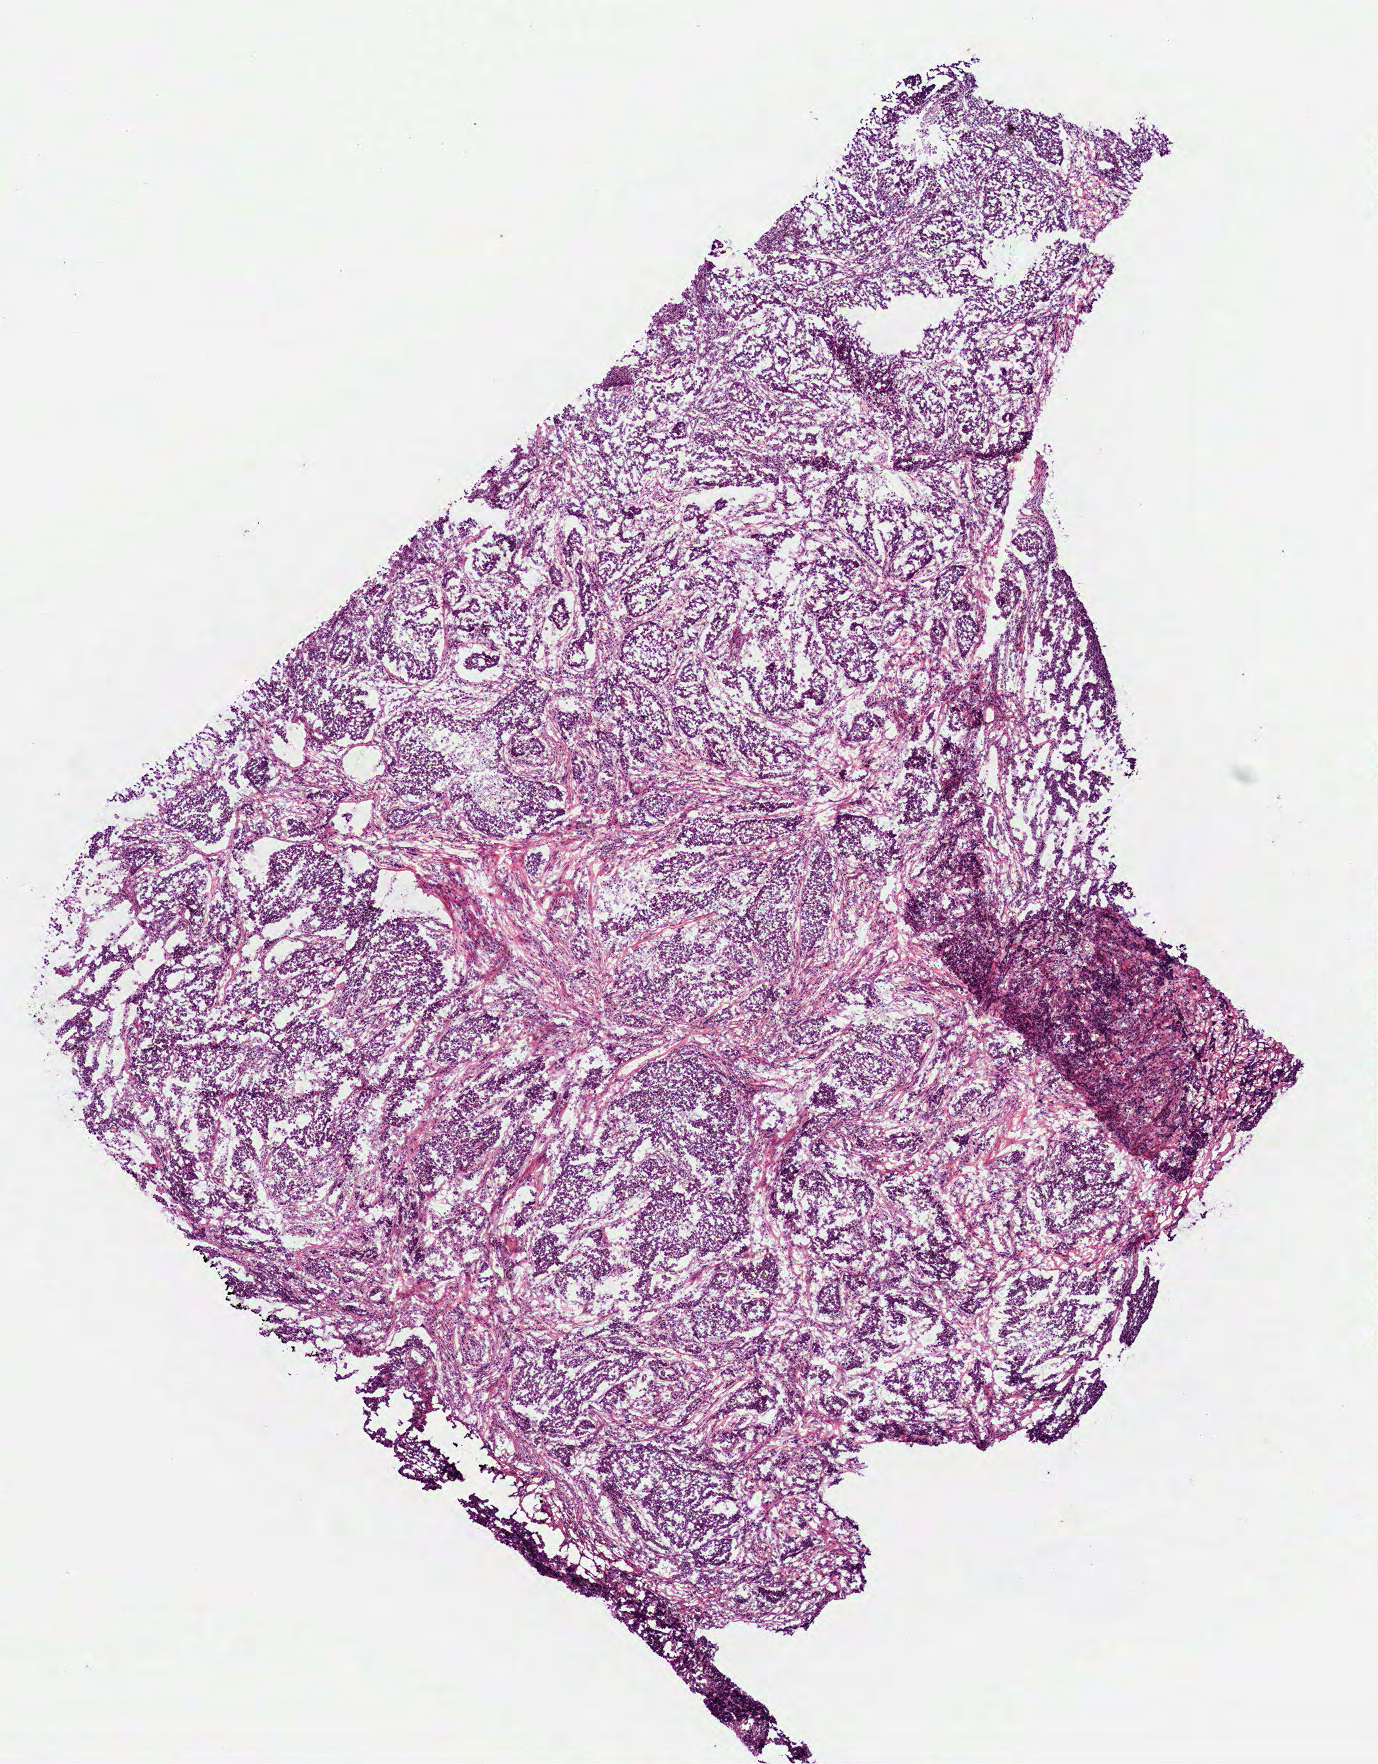
Whole-slide histology image, H&E-stained — low-resolution overview of the scanned area, about 5.6 x 7.1 mm (acquisition: 40x scan), frozen section, lung, primary tumour sample. Male patient; age at initial diagnosis 69 years. Composition of this section per pathologist review: tumour cells 100%, tumour nuclei 75%, normal cells 0%, stromal cells 0%, necrosis 0%. Infiltration values recorded for this section: lymphocyte infiltration 10%, monocyte infiltration 5%, neutrophil infiltration 5%.
Laterality: right. Histologic diagnosis: Adenocarcinoma, NOS (upper lobe, lung). TNM: T2 N2 M0. AJCC pathologic stage: IIIA (6th edition).